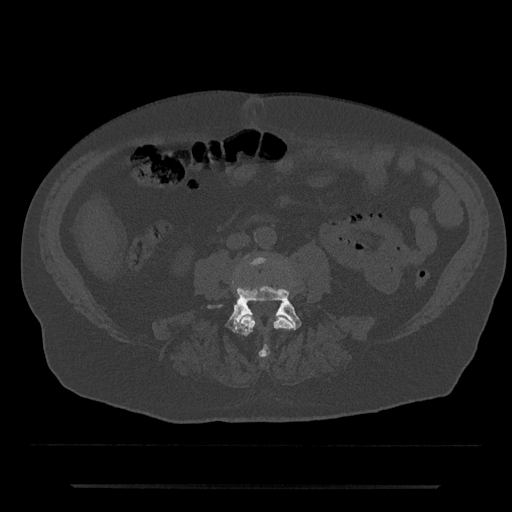
CT including the spine, one axial slice; slice 372 of 797 in the series (ordered by position); 120 kVp; bone window (W 1800 / L 400 HU); 0.5 mm slice thickness; 512 × 512 image matrix. Patient: male, 80 years. Case-level facts recorded for this patient, not image findings: primary cancer: prostate; vertebrae with lytic lesions (as recorded): L1, T11.
Outlined on this slice (semi-automatically segmented with operator editing):
- L3 vertebra: bounding box (x1, y1, x2, y2) in pixels: (237, 256, 294, 357)
- L4 vertebra: (208, 285, 302, 333)